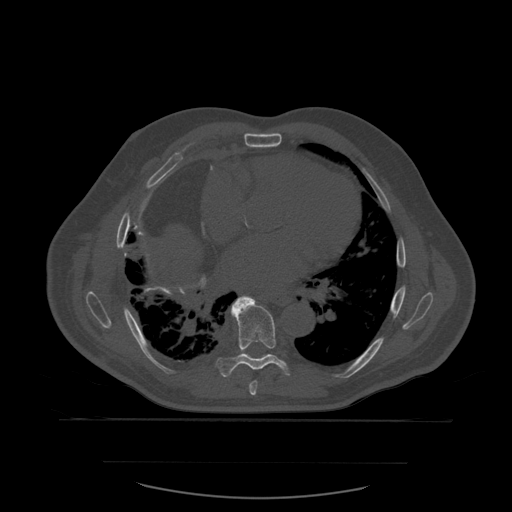
CT including the spine, one axial slice. Position 363 of 590 along the scan axis. Bone window (W 1800 / L 400 HU). 512 × 512 image matrix. Patient age 71 years. From the clinical record (not read from this slice): primary cancer: lung.
Annotated regions visible in this slice (semi-automatically segmented with operator editing):
- T7 vertebra: bounding box (x1, y1, x2, y2) in pixels: (249, 381, 258, 396)
- T8 vertebra: (218, 296, 292, 377)